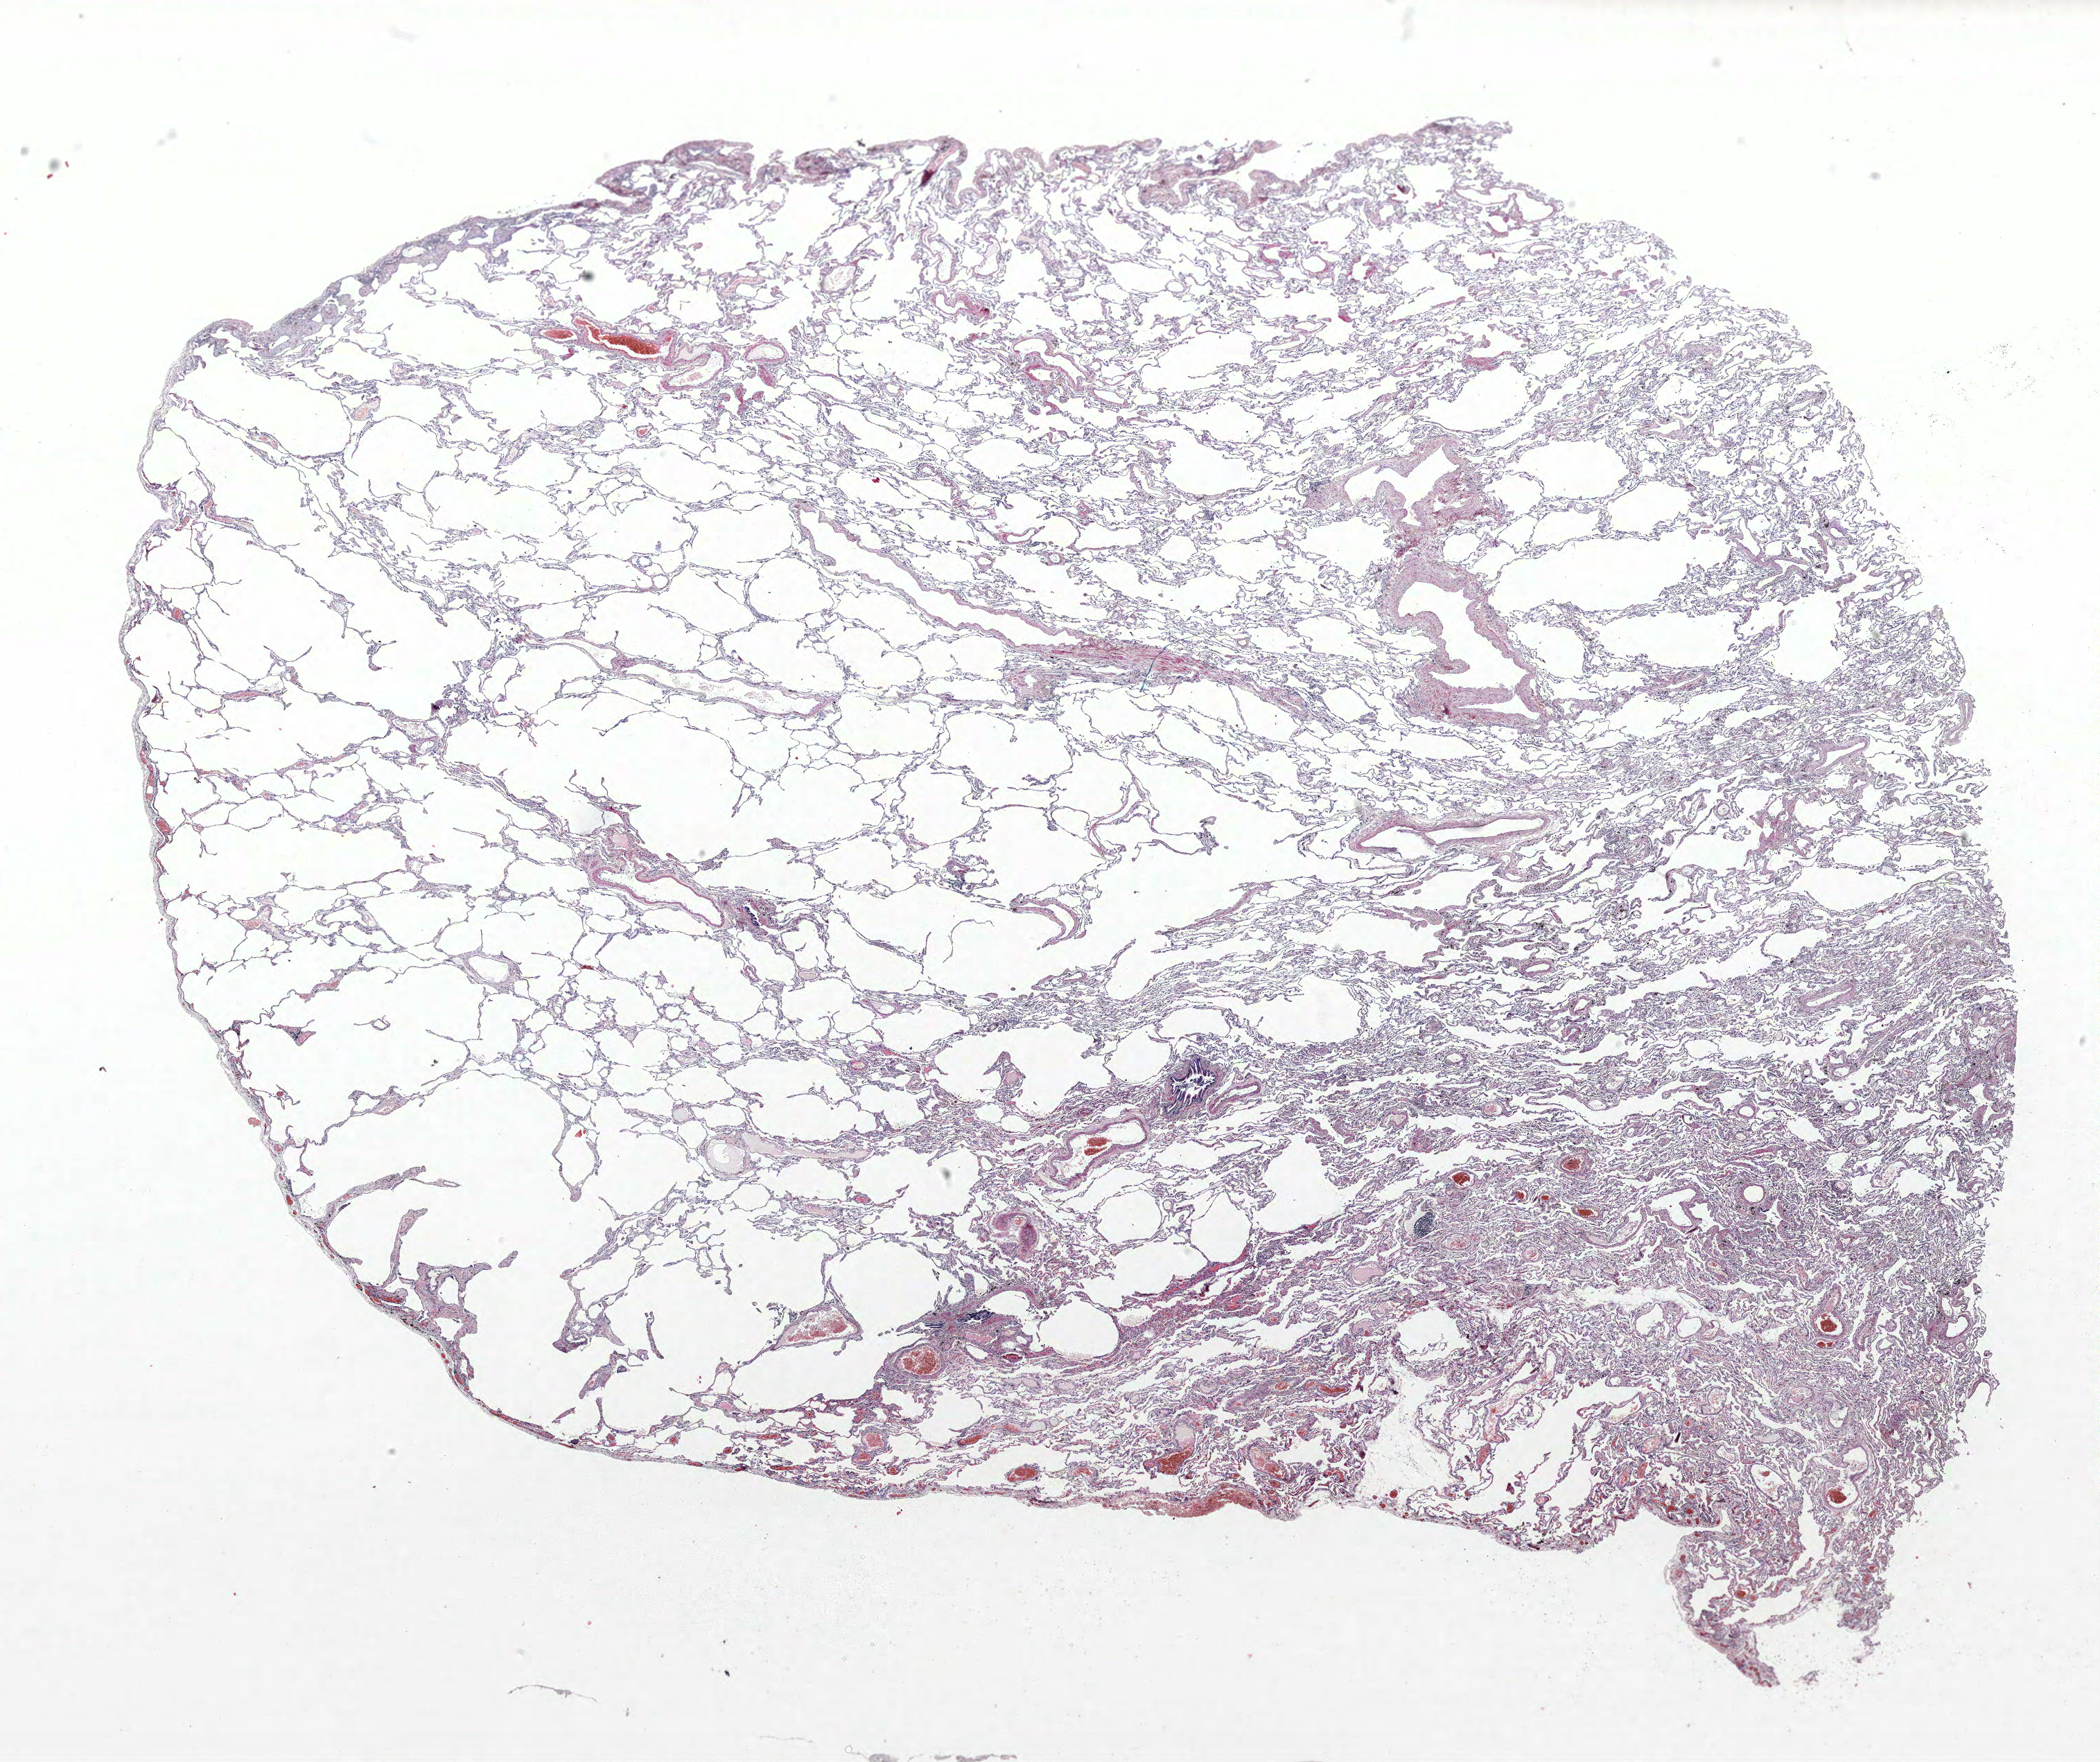
Whole-slide histology image, Hematoxylin and eosin (H&E) stained, whole scanned area (about 24.2 x 20.3 mm, from a 40x scan) shown as a low-resolution overview. FFPE section. Lung tissue. Male, age 66 at enrolment. Current smoker at enrolment.
- ICD-O-3 topography: upper lobe of lung (C34.1)
- tumour size (pathology): 23 mm
- participant's lung-cancer diagnosis: Squamous cell carcinoma, NOS
- primary tumour location (clinical record): left upper lobe
- stage (AJCC 6th edition): IA
- note: participant had 2 primary lung cancers recorded; fields above describe the first